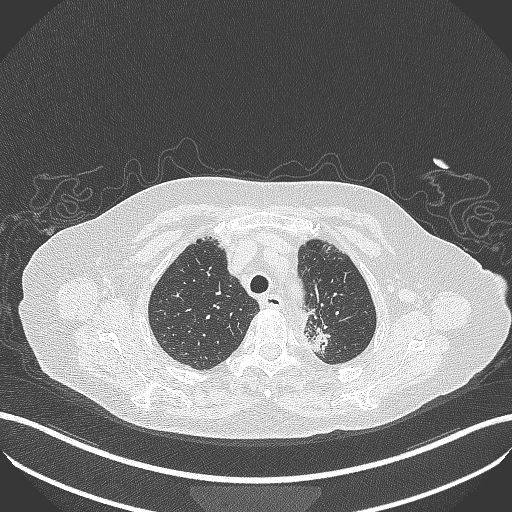
Chest CT, one axial slice. Position 277 of 353 along the scan axis. 100 kVp. Lung window (W 1500 / L -600 HU). 1 mm slice thickness. 512 × 512 image matrix, field of view 400 × 400 mm. Patient: female, 81 years. Case-level facts recorded for this patient, not image findings: clinical TNM (as recorded): T2a N0 M0.
Structures marked on this image (rectangle marked by the reading radiologist):
- lung tumour (recorded histology: adenocarcinoma): box from (x=294, y=301) to (x=331, y=358) px